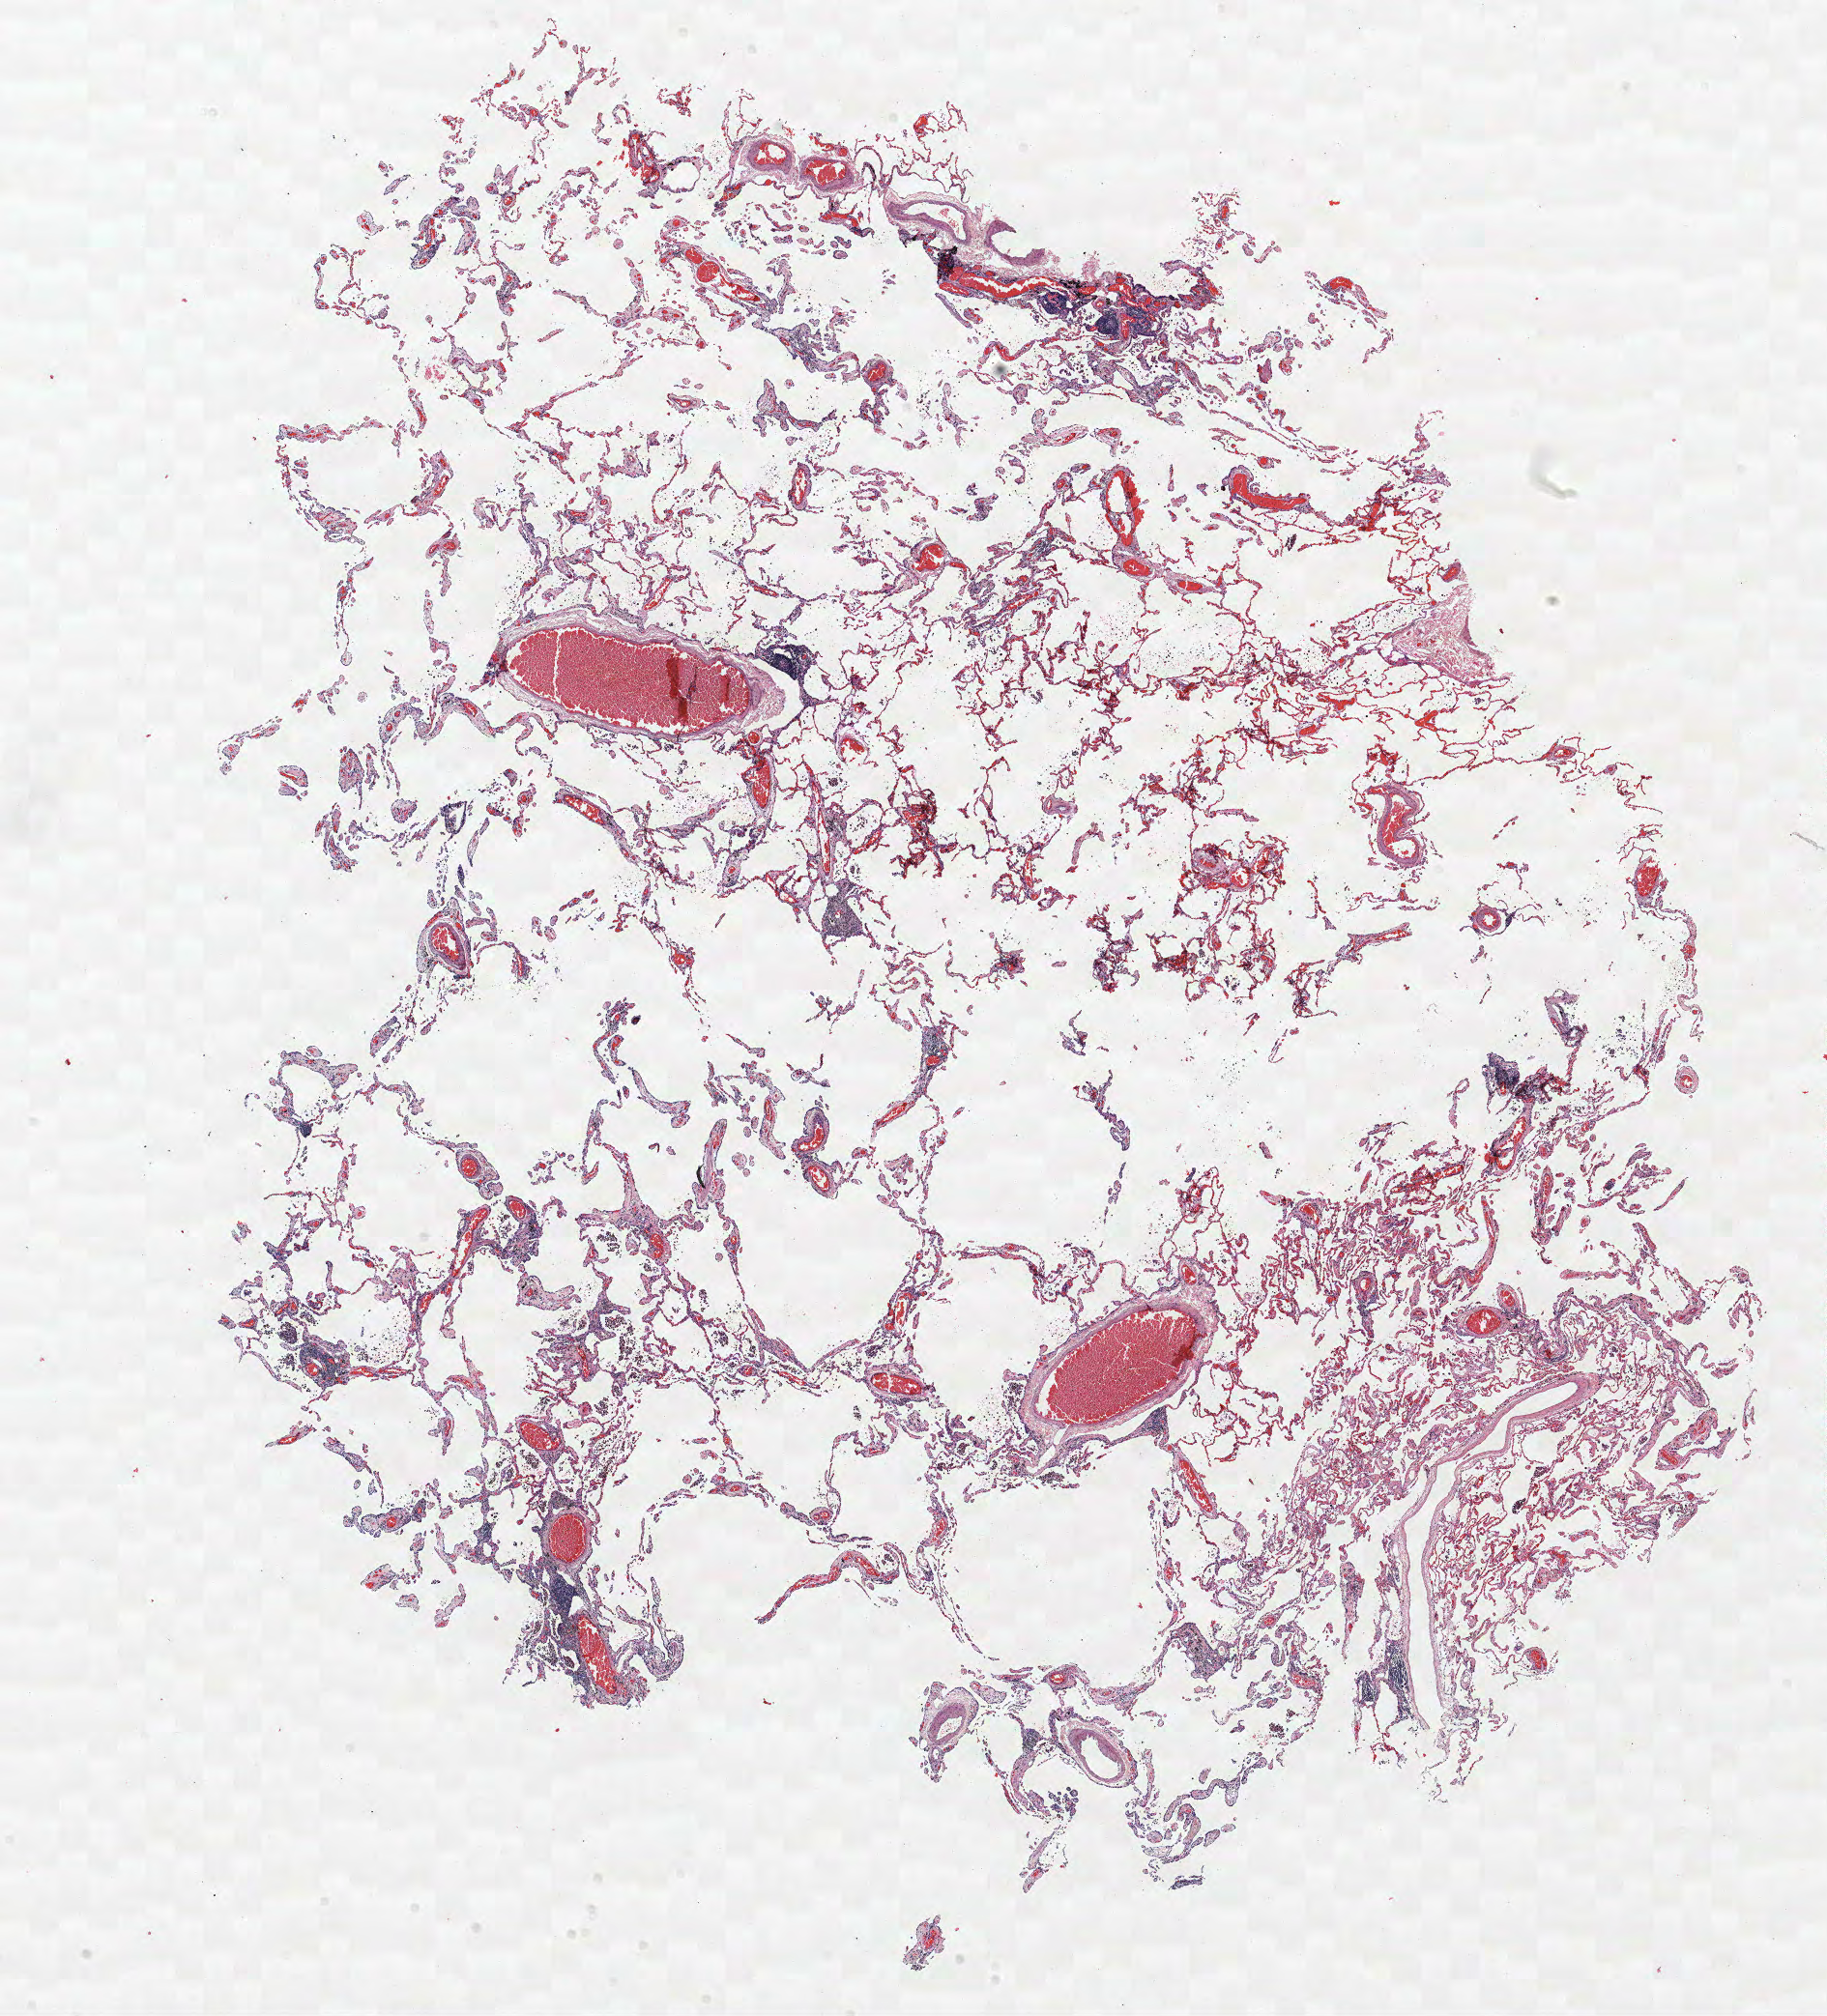
Whole-slide histology image, H&E — a low-resolution overview of the entire scanned area, about 15.1 x 16.7 mm (from a 40x scan); formalin-fixed paraffin-embedded (FFPE) section; lung tissue. Male, age 62 at enrolment. Grade: moderately differentiated (G2).
- participant's lung-cancer diagnosis: Bronchiolo-alveolar adenocarcinoma, NOS (ICD-O-3 8250/3)
- stage (AJCC 6th edition): IIA
- tumour size (pathology): 11 mm
- primary tumour location (clinical record): right upper lobe